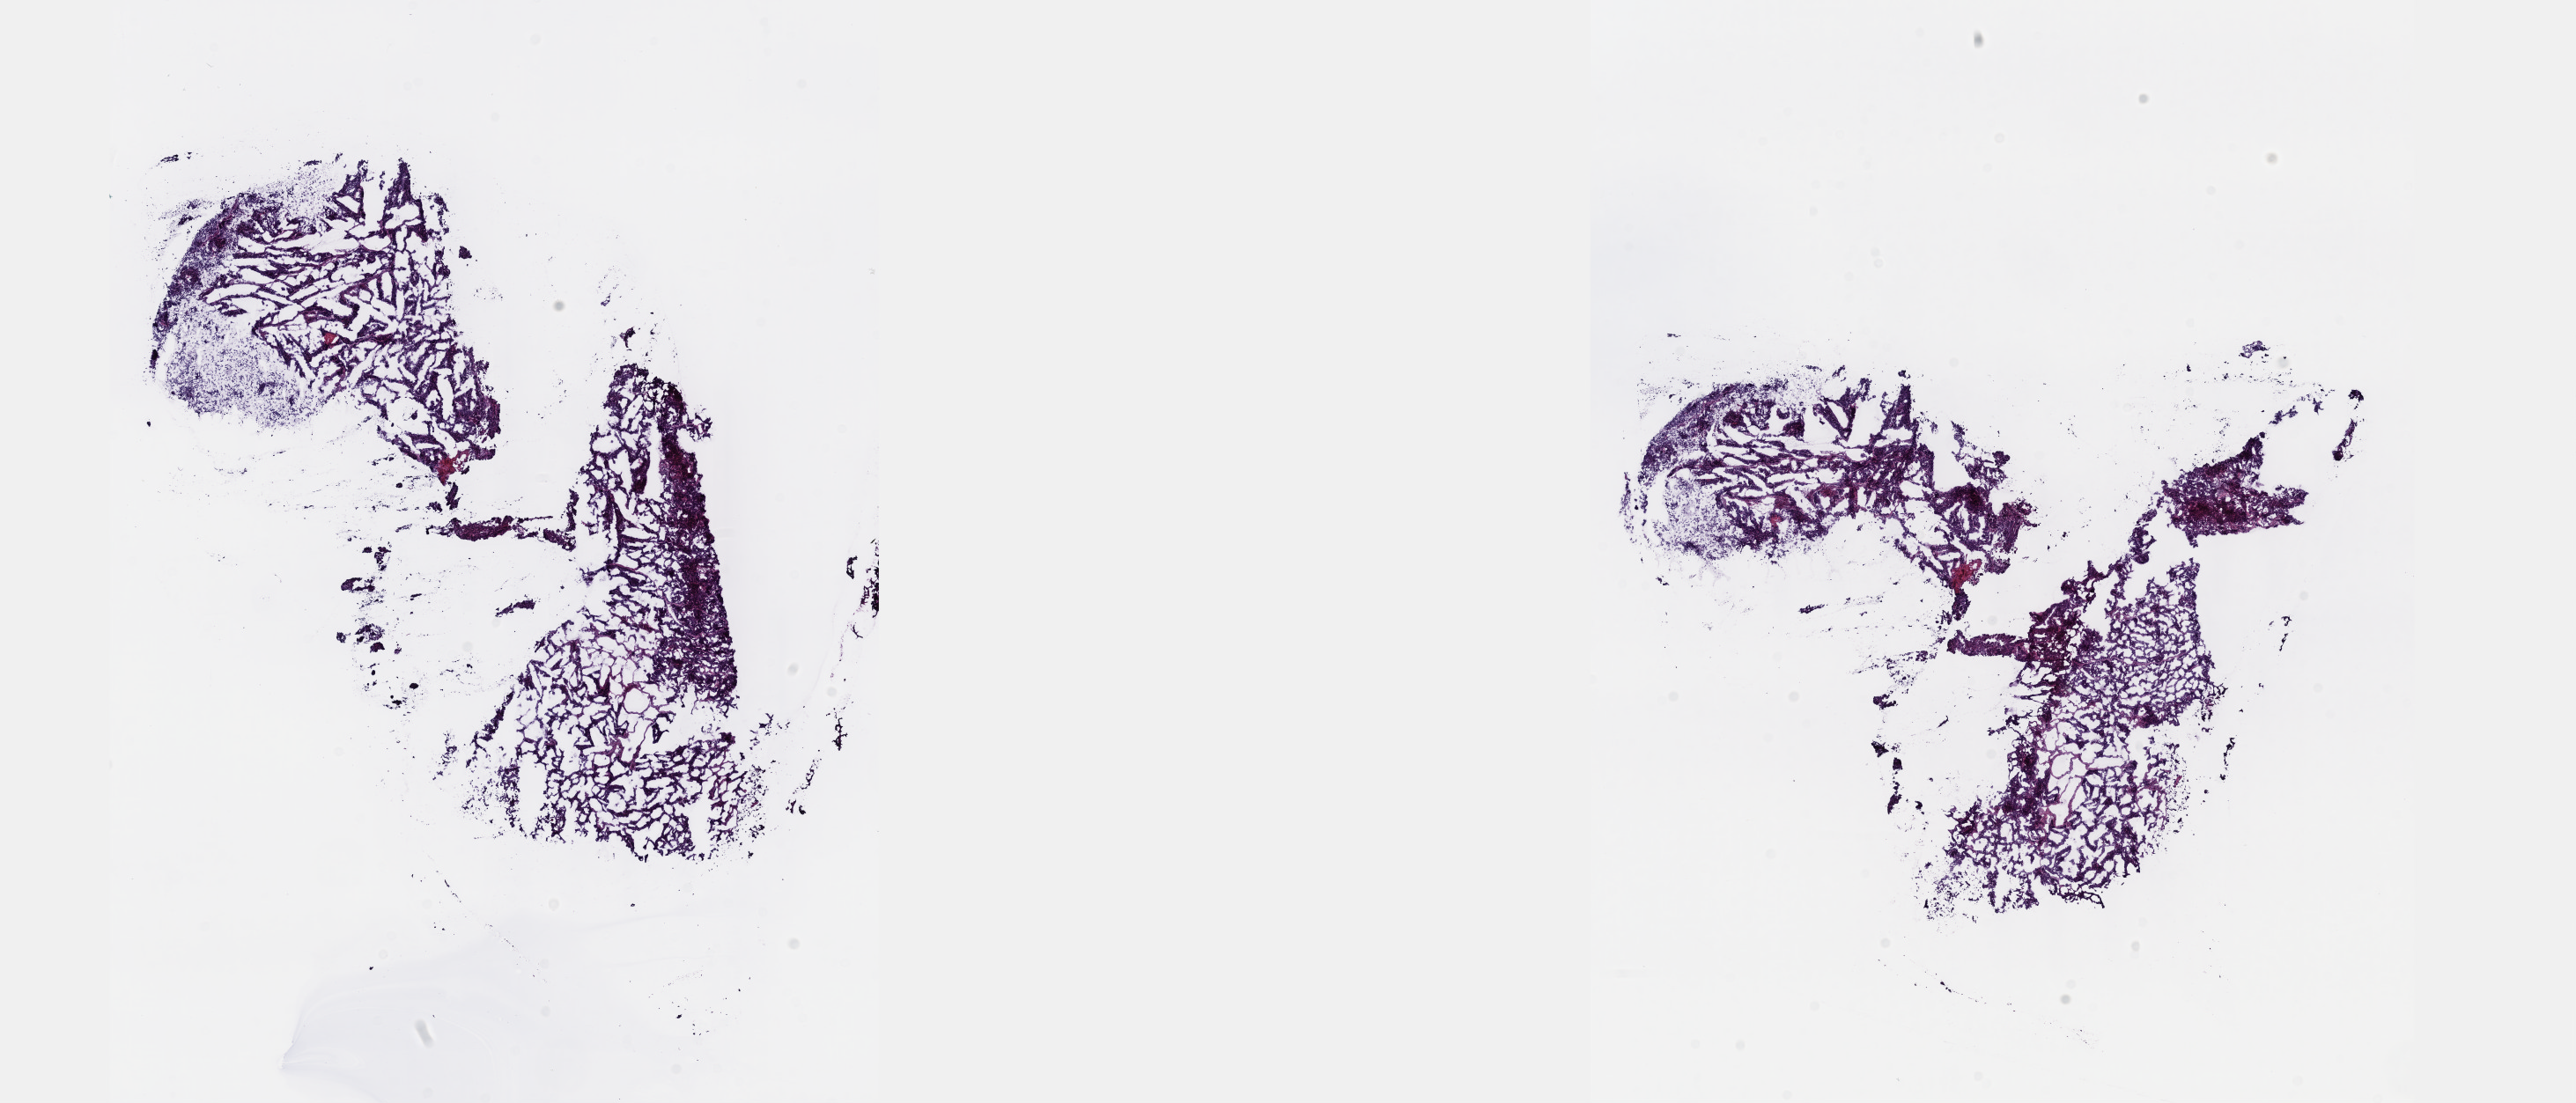
Digitized H&E-stained tissue section (whole slide), a low-resolution overview of the entire scanned area, about 23.6 x 10.1 mm (from a 40x scan); frozen section from the top of the tissue portion; primary tumour sample from the uterus. Female patient; age at initial diagnosis 60 years. Histologic grade: G3 (poorly differentiated). Pathologist review of this section (percent, as recorded): tumour cells 90%, tumour nuclei 95%, normal cells 0%, stromal cells 10%, necrosis 0%. Inflammatory infiltration, as recorded: lymphocyte infiltration 0%, monocyte infiltration 0%, neutrophil infiltration 0%.
FIGO stage: IA. Pathologic diagnosis: Serous surface papillary carcinoma (endometrium).